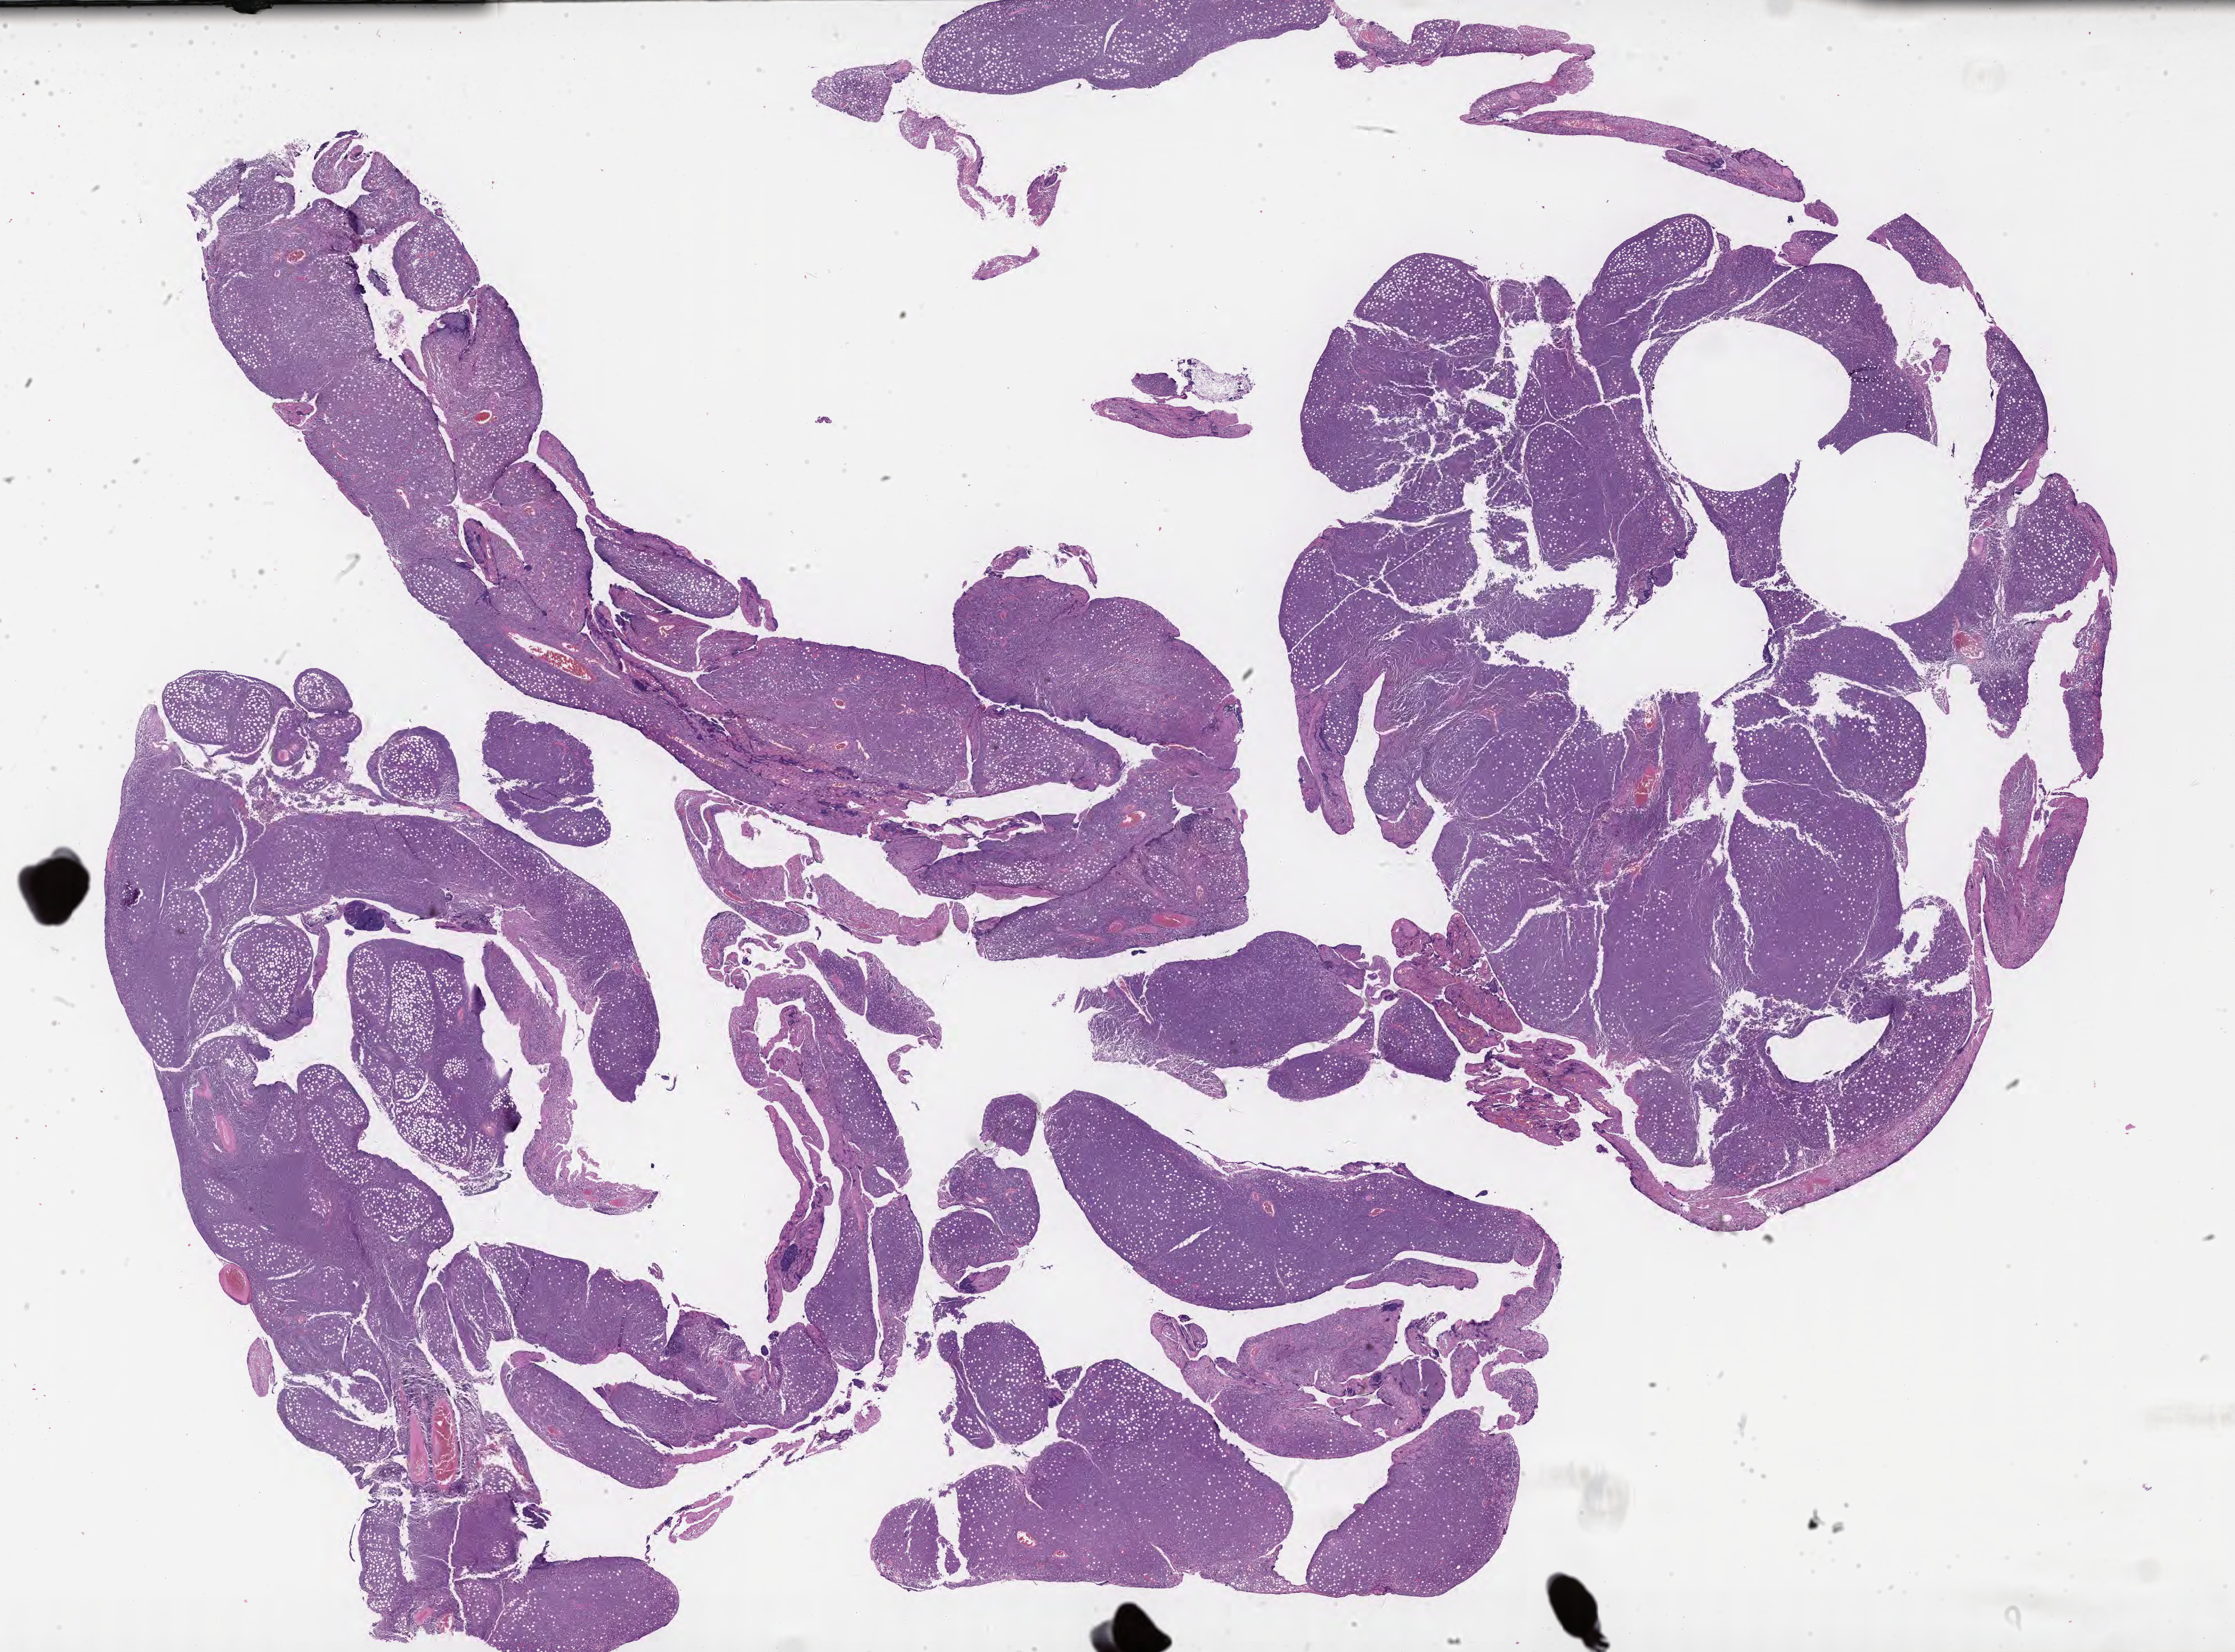
Whole-slide image, haematoxylin and eosin stain, shown as a low-resolution overview of the whole scanned area (about 31.7 x 23.4 mm); specimen: tumor tissue. Male, age 8 years at initial diagnosis.
• diagnosis: Burkitt lymphoma, NOS